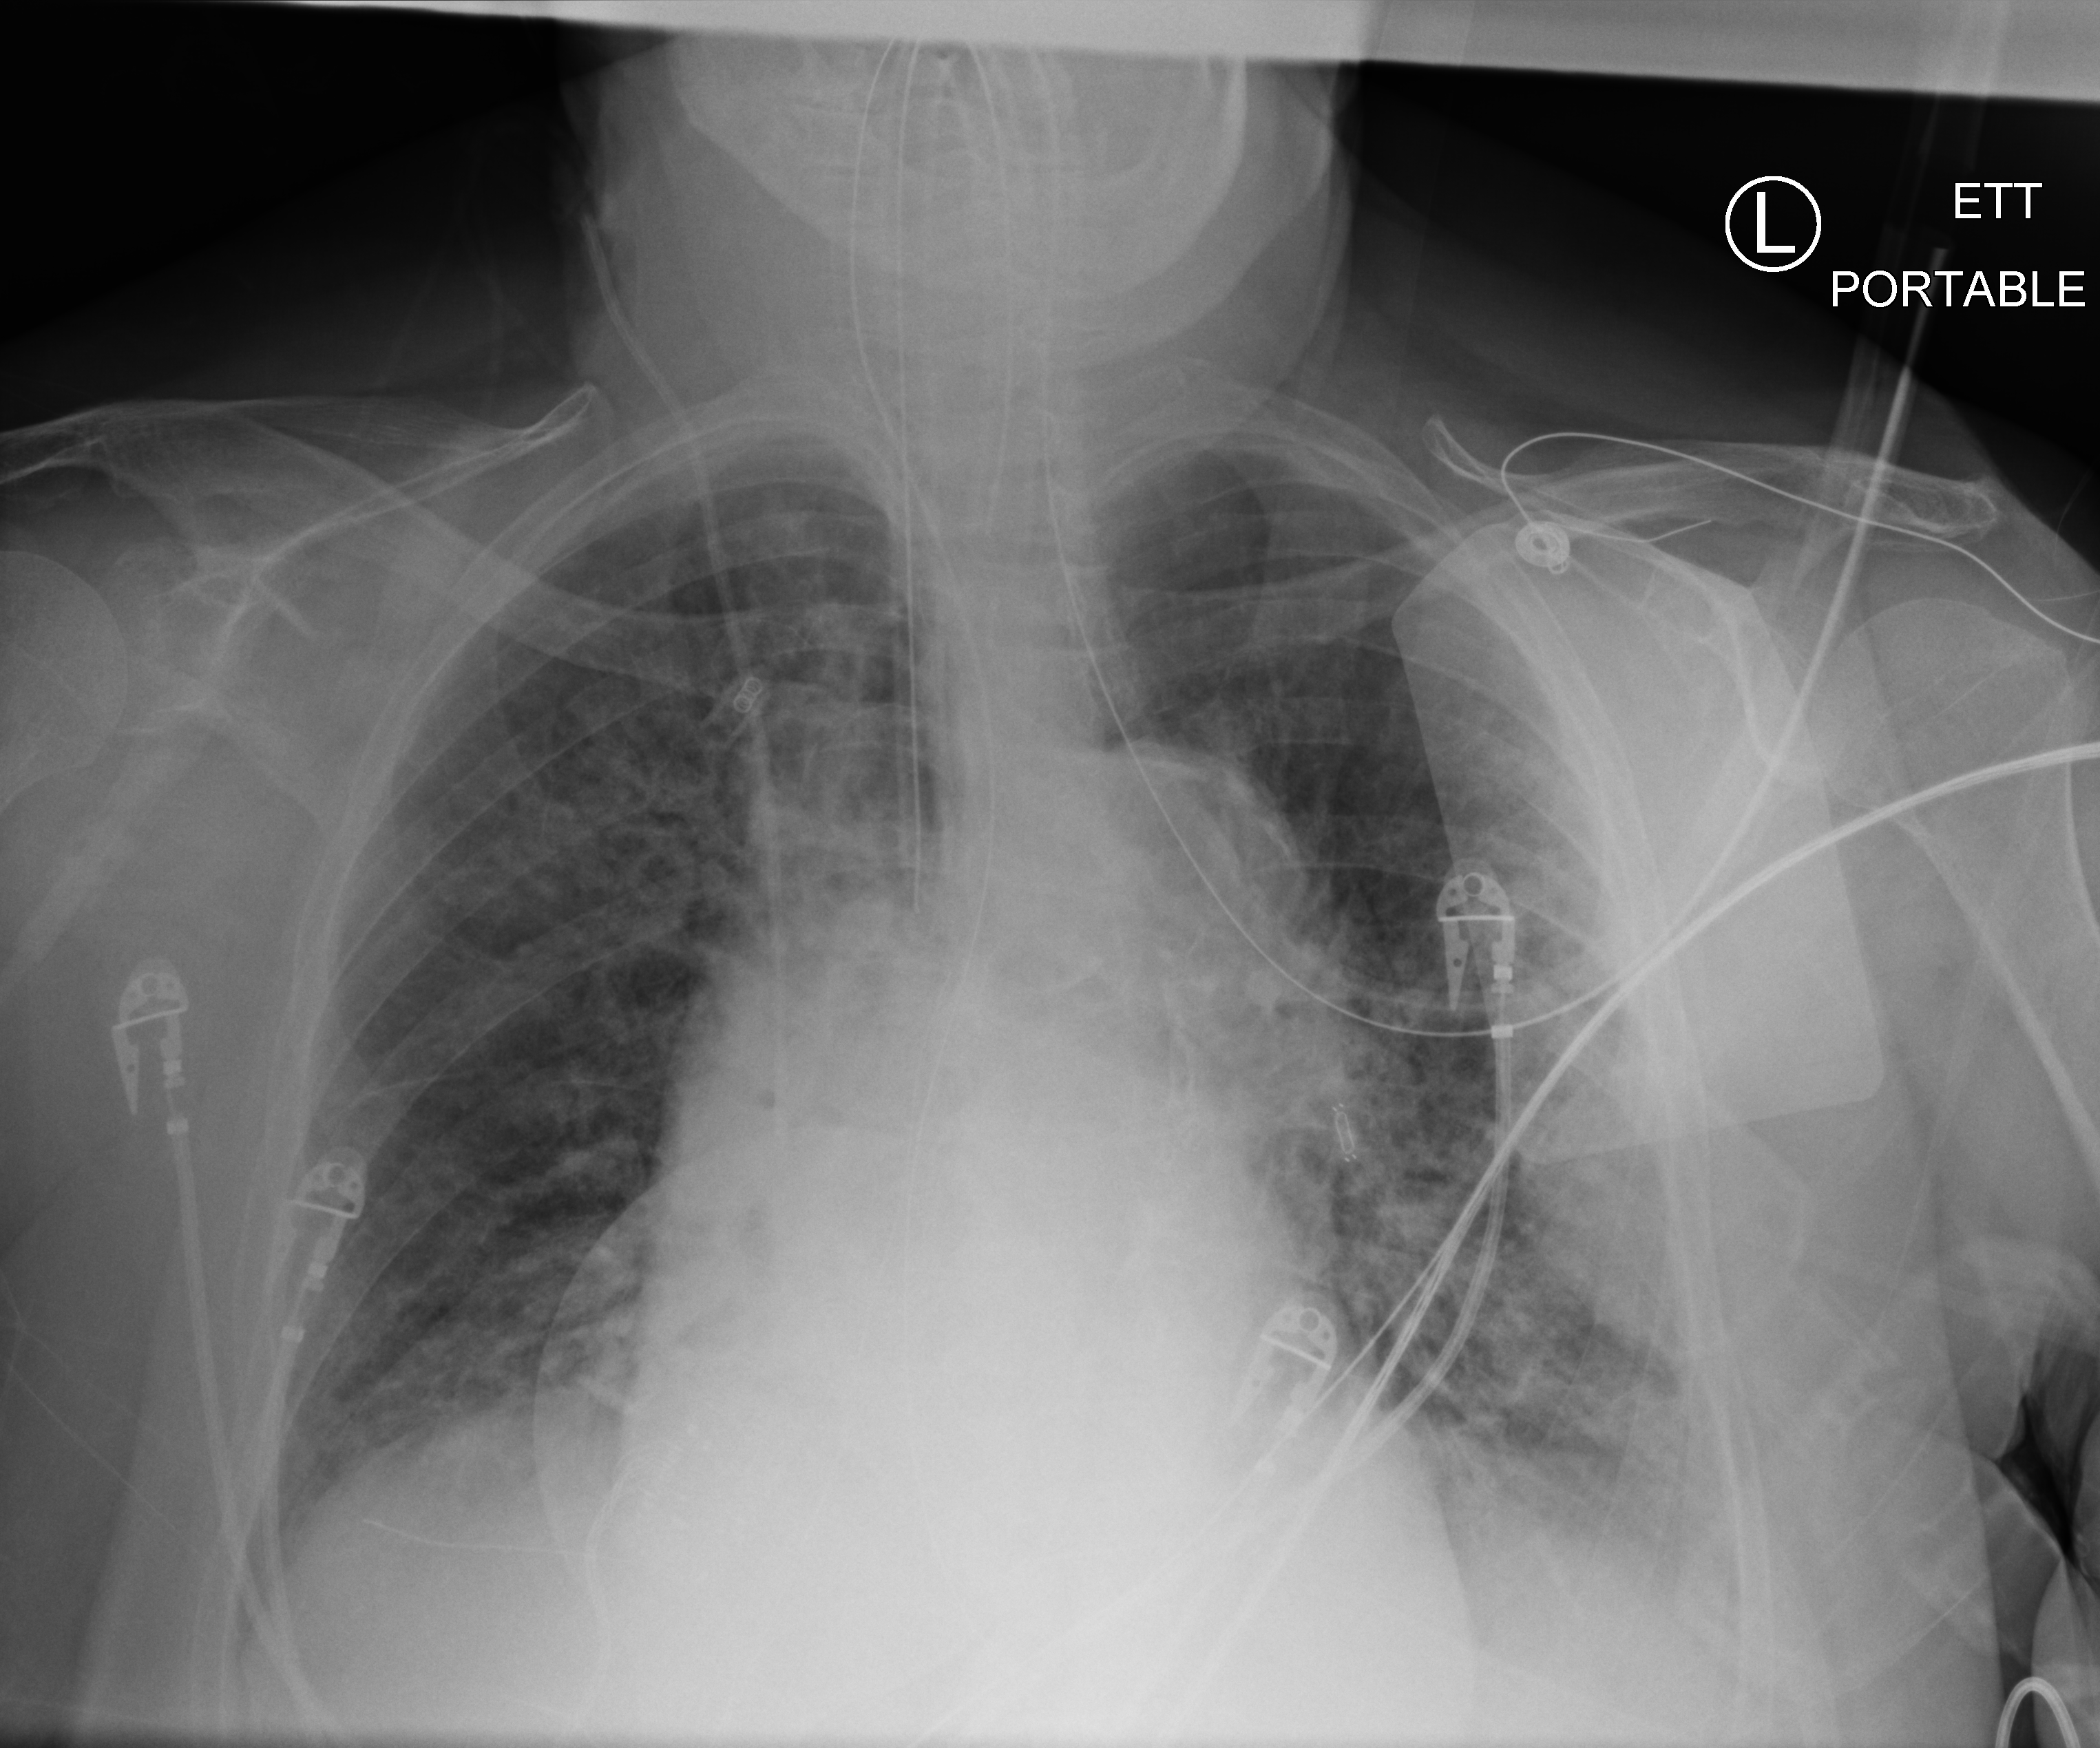
Portable chest radiograph; anteroposterior (AP) projection. Patient hospitalised with COVID-19; female, aged 75–90 years.
From the hospital-stay record, not from the radiograph (when in the stay this image was taken is not recorded): admitted to intensive care during this hospital stay: yes; hypertension (admission record): yes.